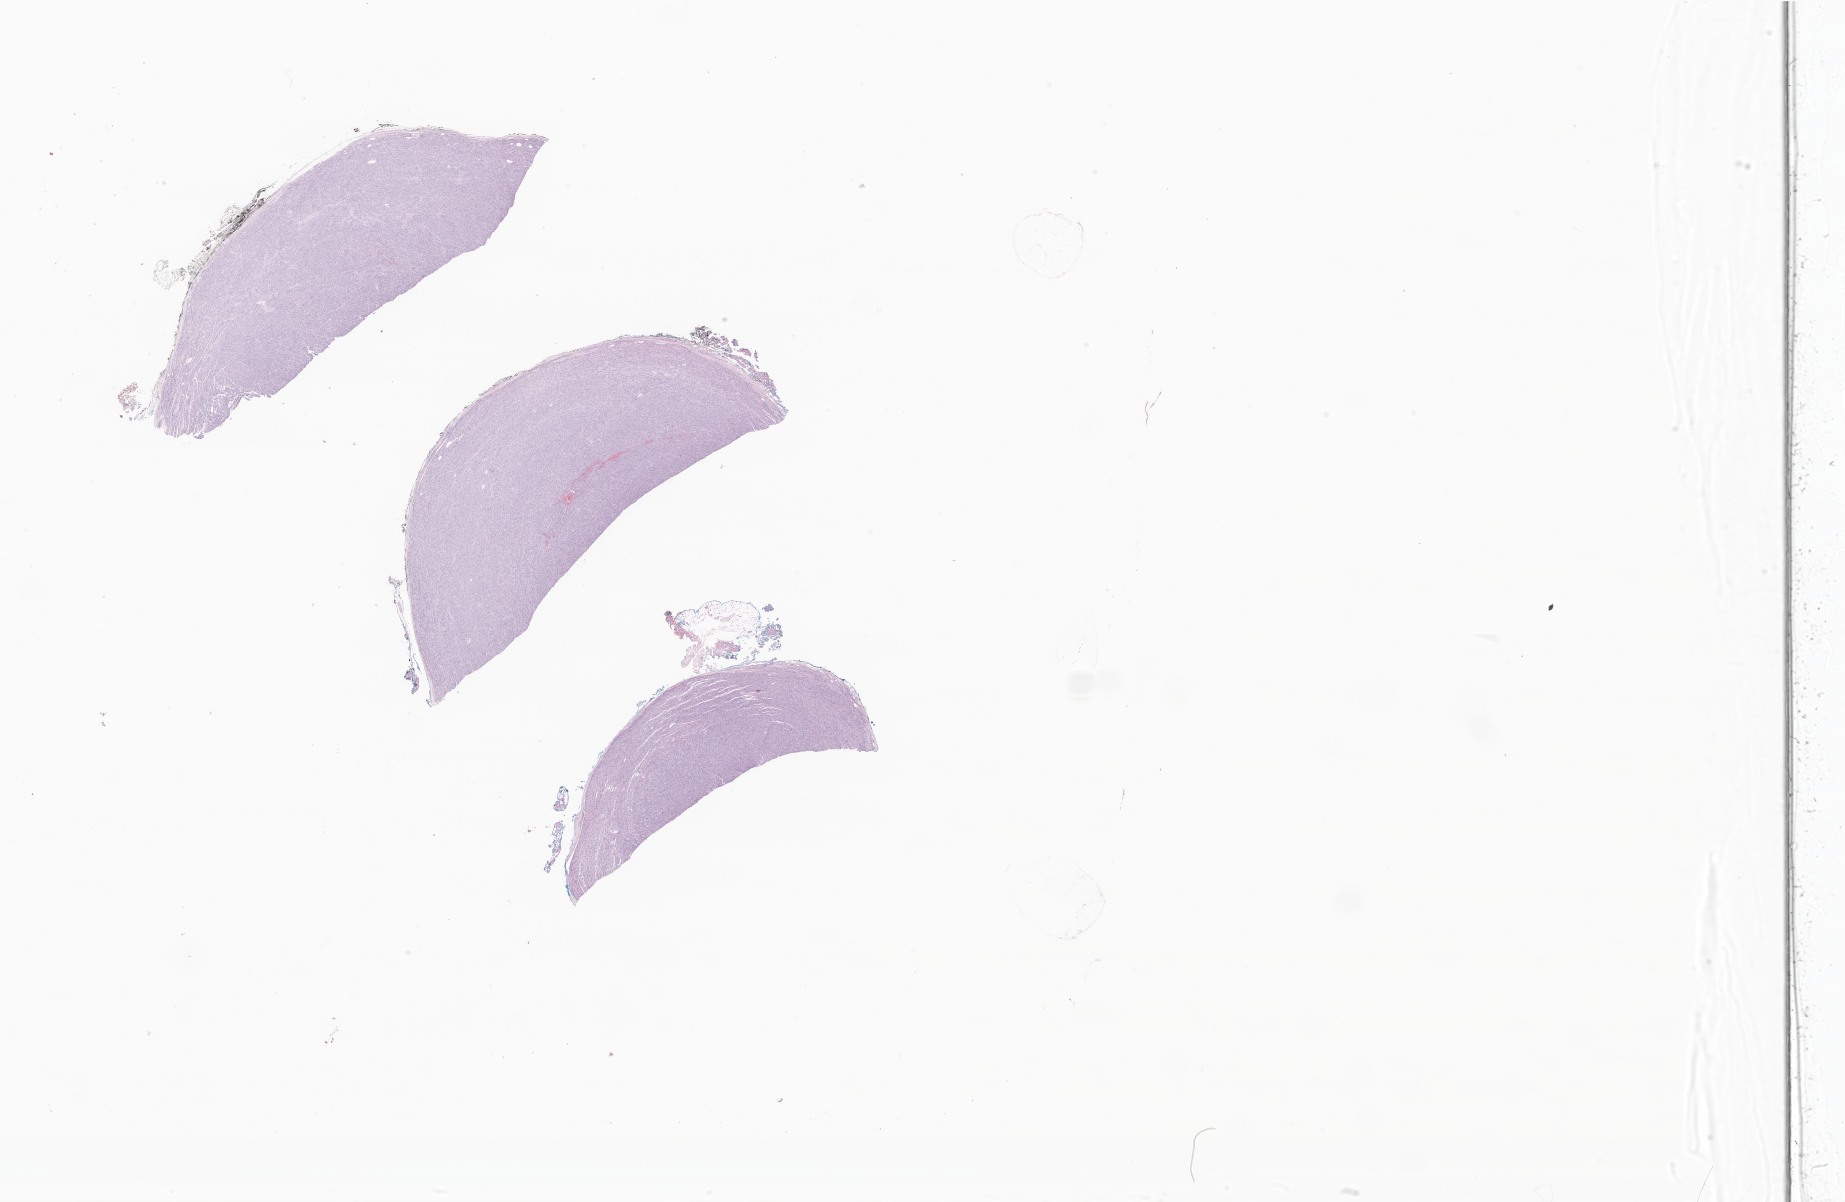
Digitized H&E-stained section of tumor tissue from the soft tissue of upper extremity — whole scanned area (about 31.1 x 20.3 mm) shown as a low-resolution overview; formalin-fixed, paraffin-embedded (FFPE) tissue. Patient female; age 64 months (5 years 4 months).
Diagnosis: Neoplasm, uncertain whether benign or malignant. Tissue or organ of origin (case record): connective, subcutaneous and other soft tissues of upper limb and shoulder.